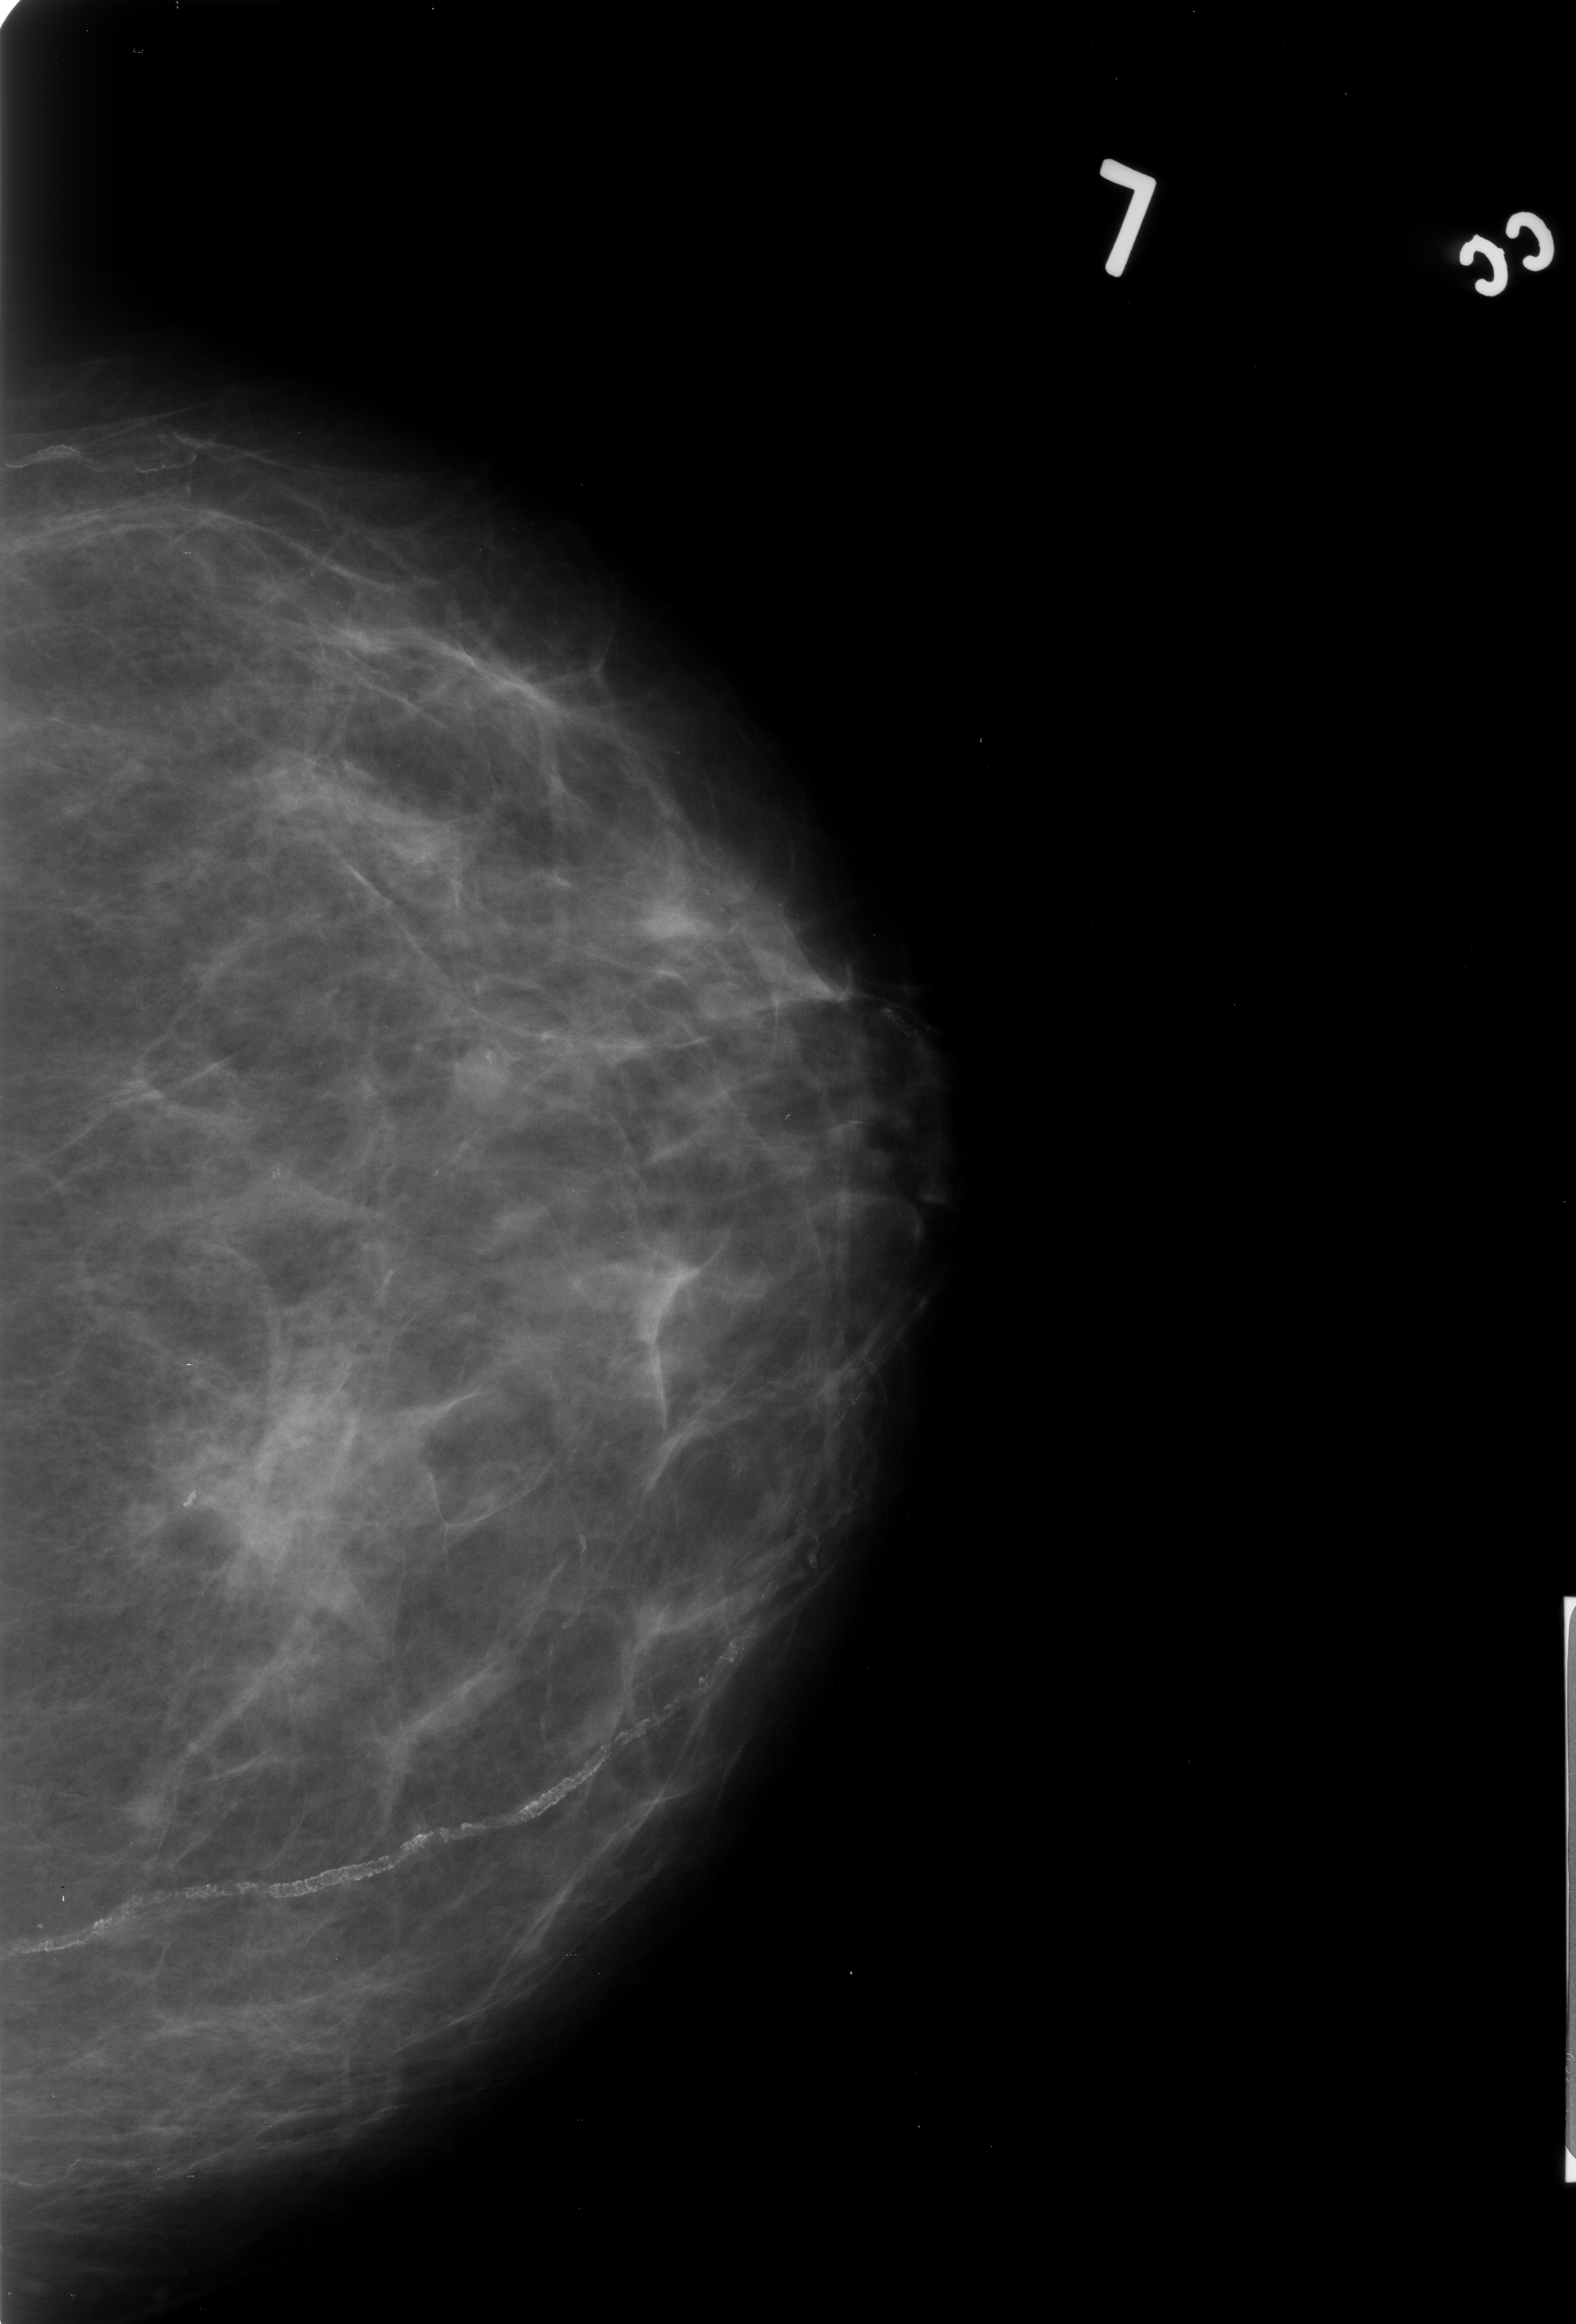
Digitized screen-film mammogram. Left breast. Craniocaudal (CC) view. BI-RADS breast density category 2 (scale 1–4). 1576 × 2324 image matrix.
Marked abnormalities (boxes around the expert regions of interest):
- Finding 1 of 2: calcifications, morphology pleomorphic, distribution clustered; BI-RADS assessment category 4; subtlety rating 2 on a 1 (subtle) to 5 (obvious) scale; pathology (as recorded): benign: bounding box (x1, y1, x2, y2) in pixels: (241, 1149, 307, 1215)
- Finding 2 of 2: calcifications, morphology pleomorphic, distribution clustered; BI-RADS assessment category 4; pathology result (as recorded, not read from the image): benign: (438, 1028, 524, 1106)